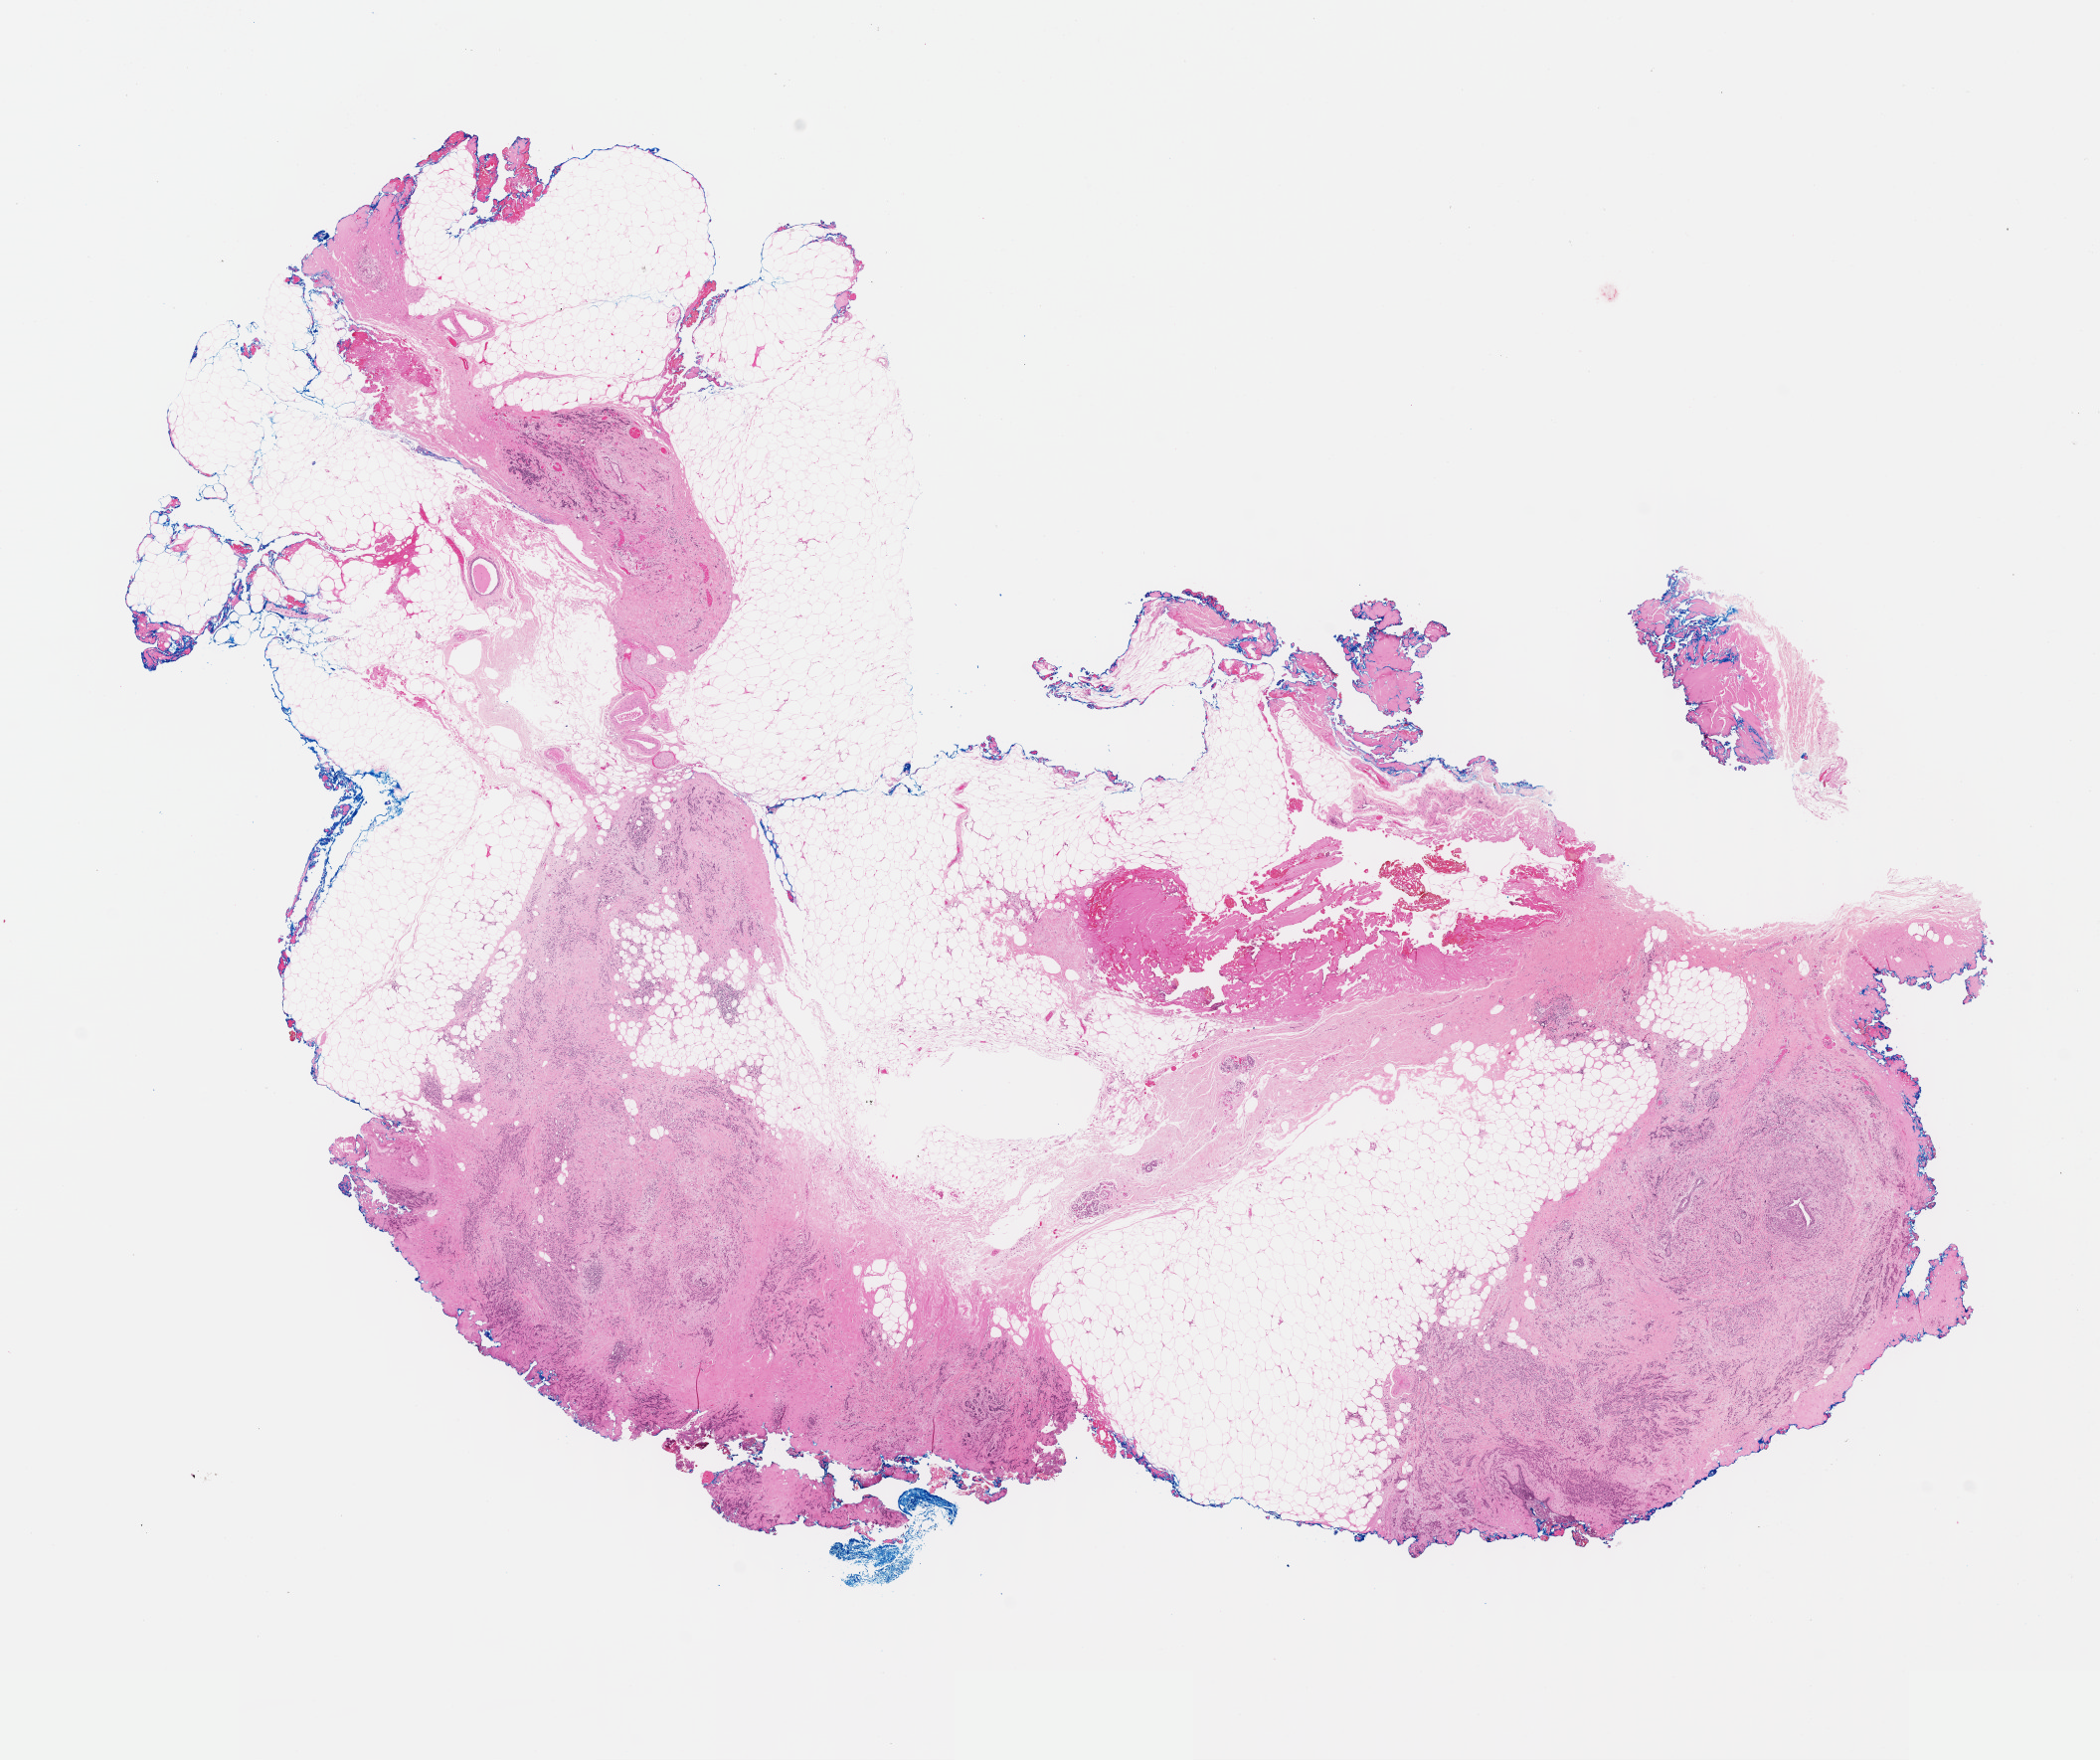
Whole-slide histology image, Hematoxylin and eosin (H&E) stained, a low-resolution overview of the entire scanned area, about 16.6 x 13.9 mm (from a 40x scan). Formalin-fixed paraffin-embedded (FFPE) diagnostic section. Sample: primary tumour, breast. Female, age 60 years at initial diagnosis.
* AJCC pathologic stage: IIIA (5th edition)
* laterality: right
* histologic diagnosis: Lobular carcinoma, NOS